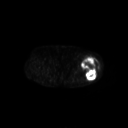
FDG PET of an extremity soft-tissue mass (from a PET/CT study), one axial slice. Slice 230 of 267 in the series (ordered by position). 3.27 mm slice thickness. 128 × 128 image matrix. Female patient, age 62 years. From the clinical record (not read from this slice): histological type: undifferentiated – high grade; grade: high; site of the primary tumour: left thigh.
Structures marked on this image (expert contour drawn on MRI and transferred to this co-registered scan by the dataset authors):
- gross tumour volume including surrounding oedema: bounding box [x1, y1, x2, y2] px = [81, 56, 99, 80]
- gross tumour volume (mass): [81, 56, 99, 80]